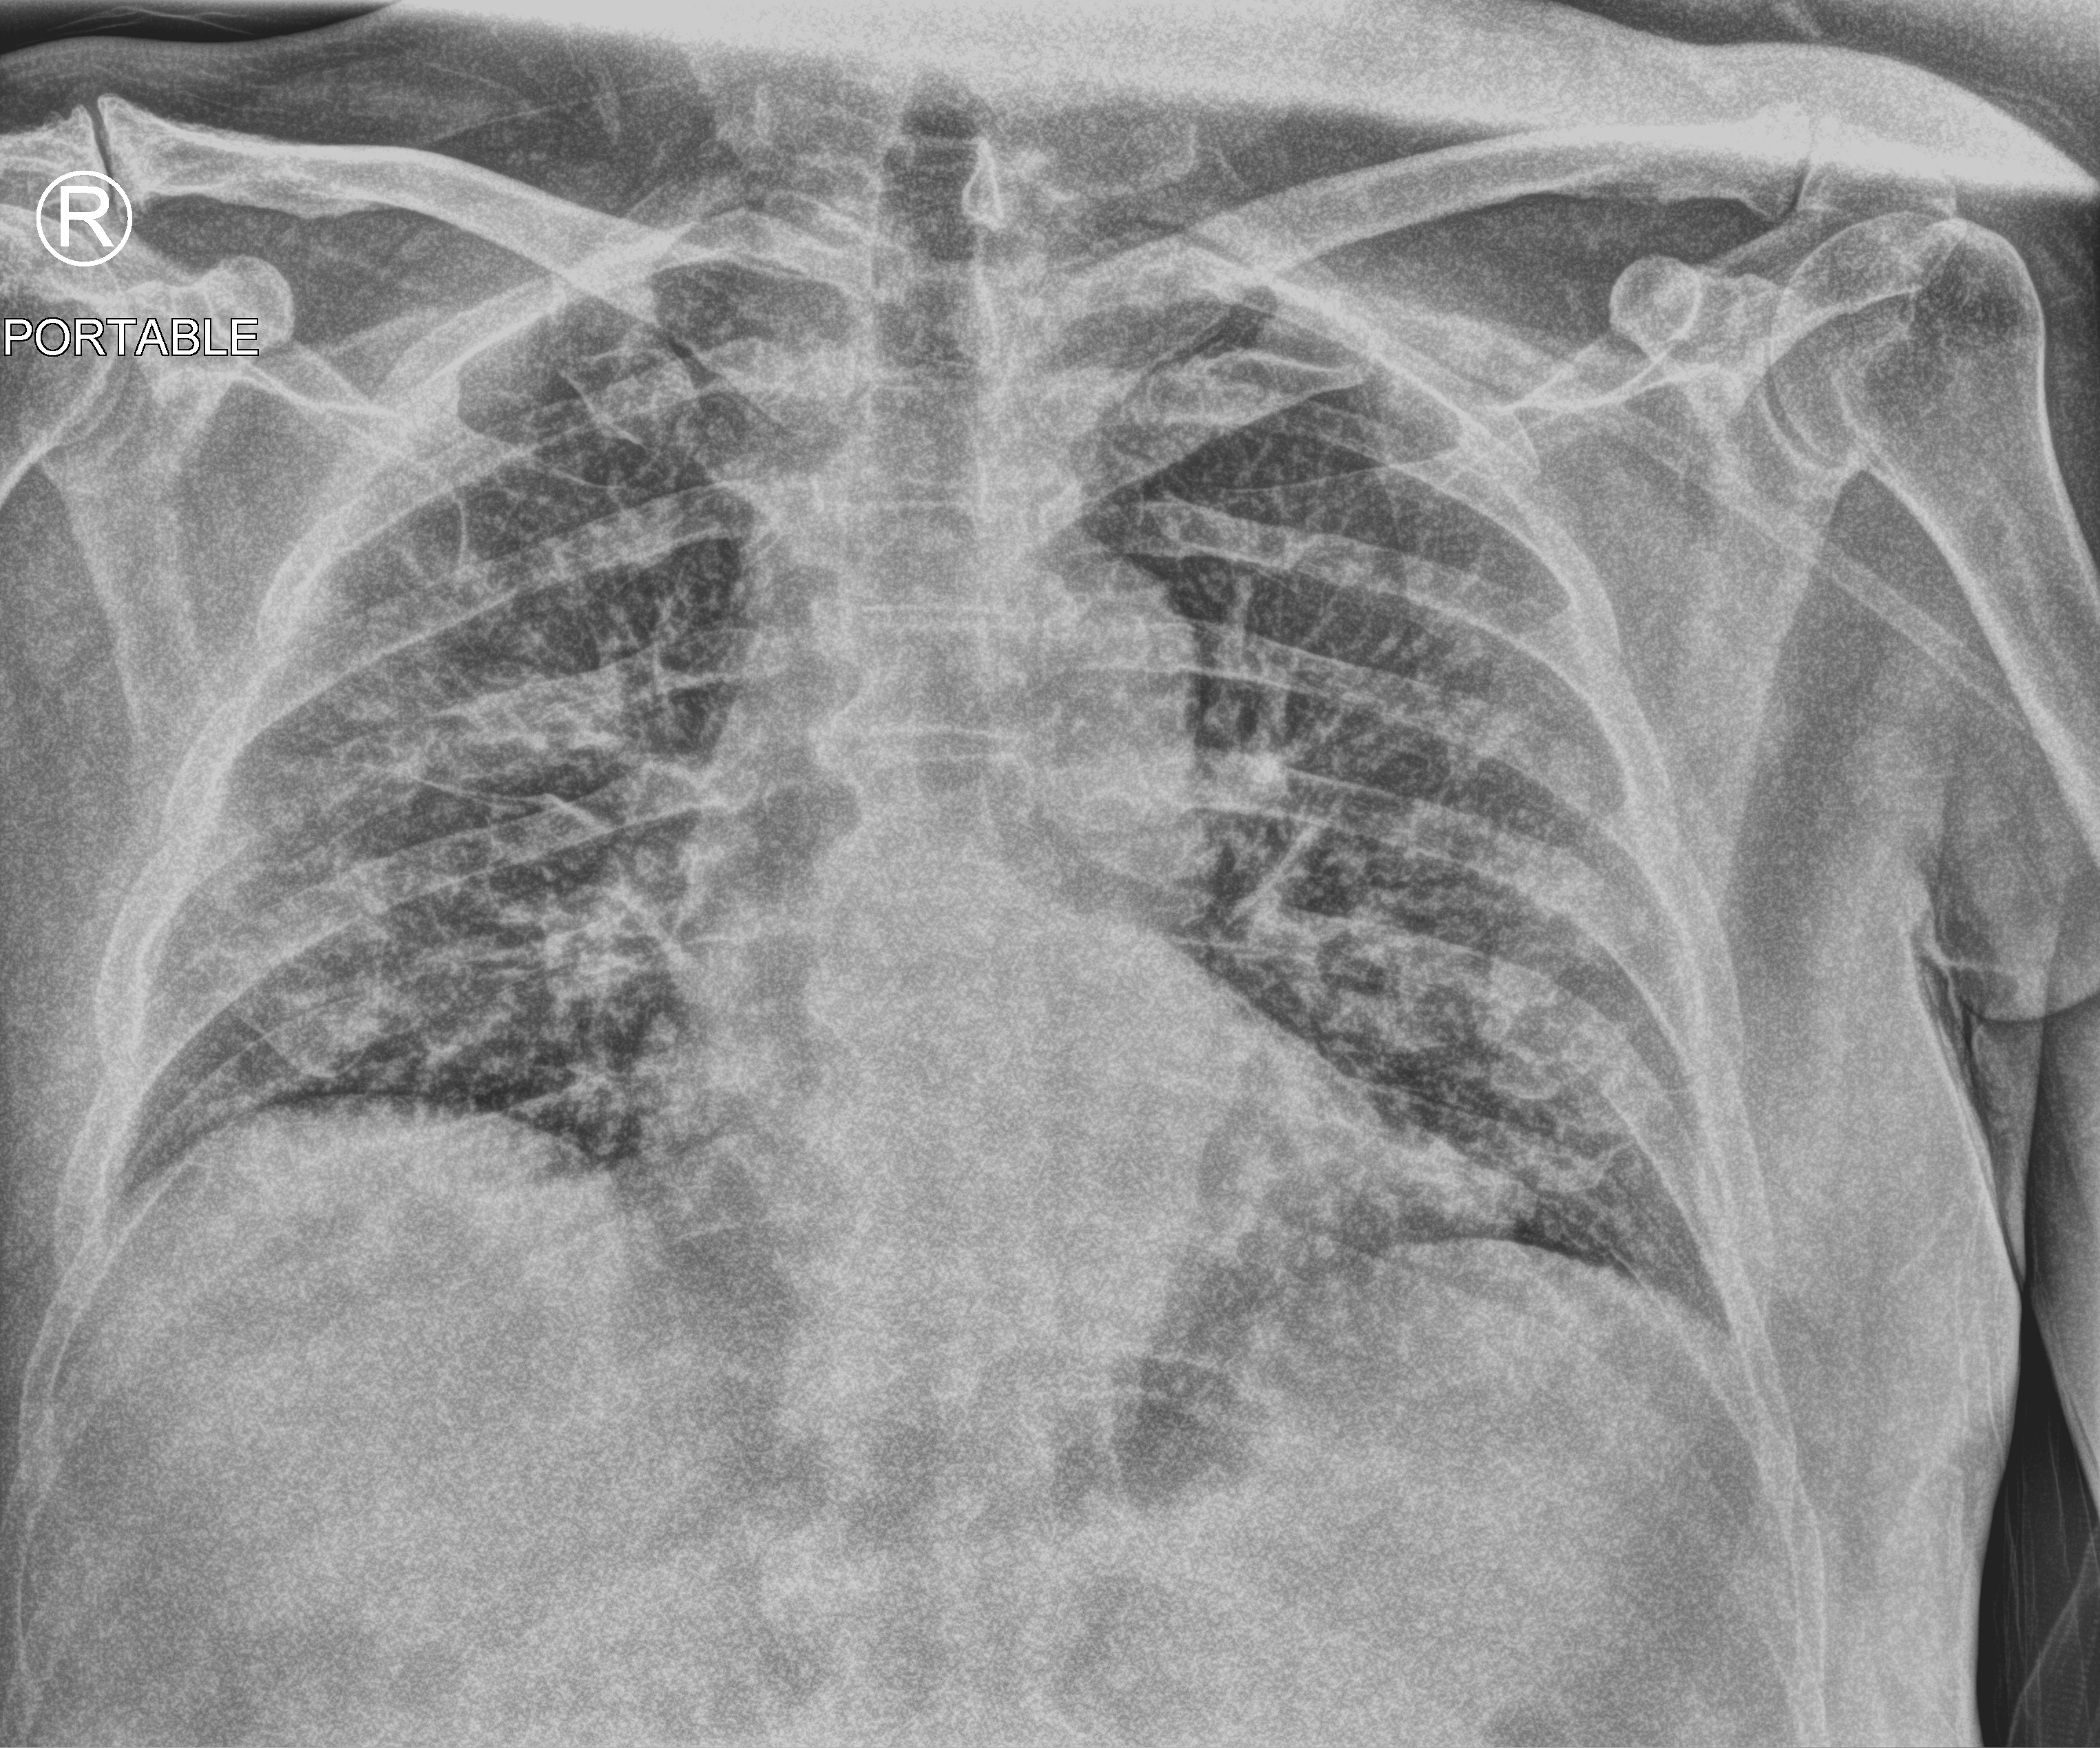
Bedside chest radiograph (computed radiography). Patient hospitalised with COVID-19; male, aged 60–74 years.
From the hospital-stay record, not from the radiograph (when in the stay this image was taken is not recorded): mechanically ventilated during this hospital stay: no.